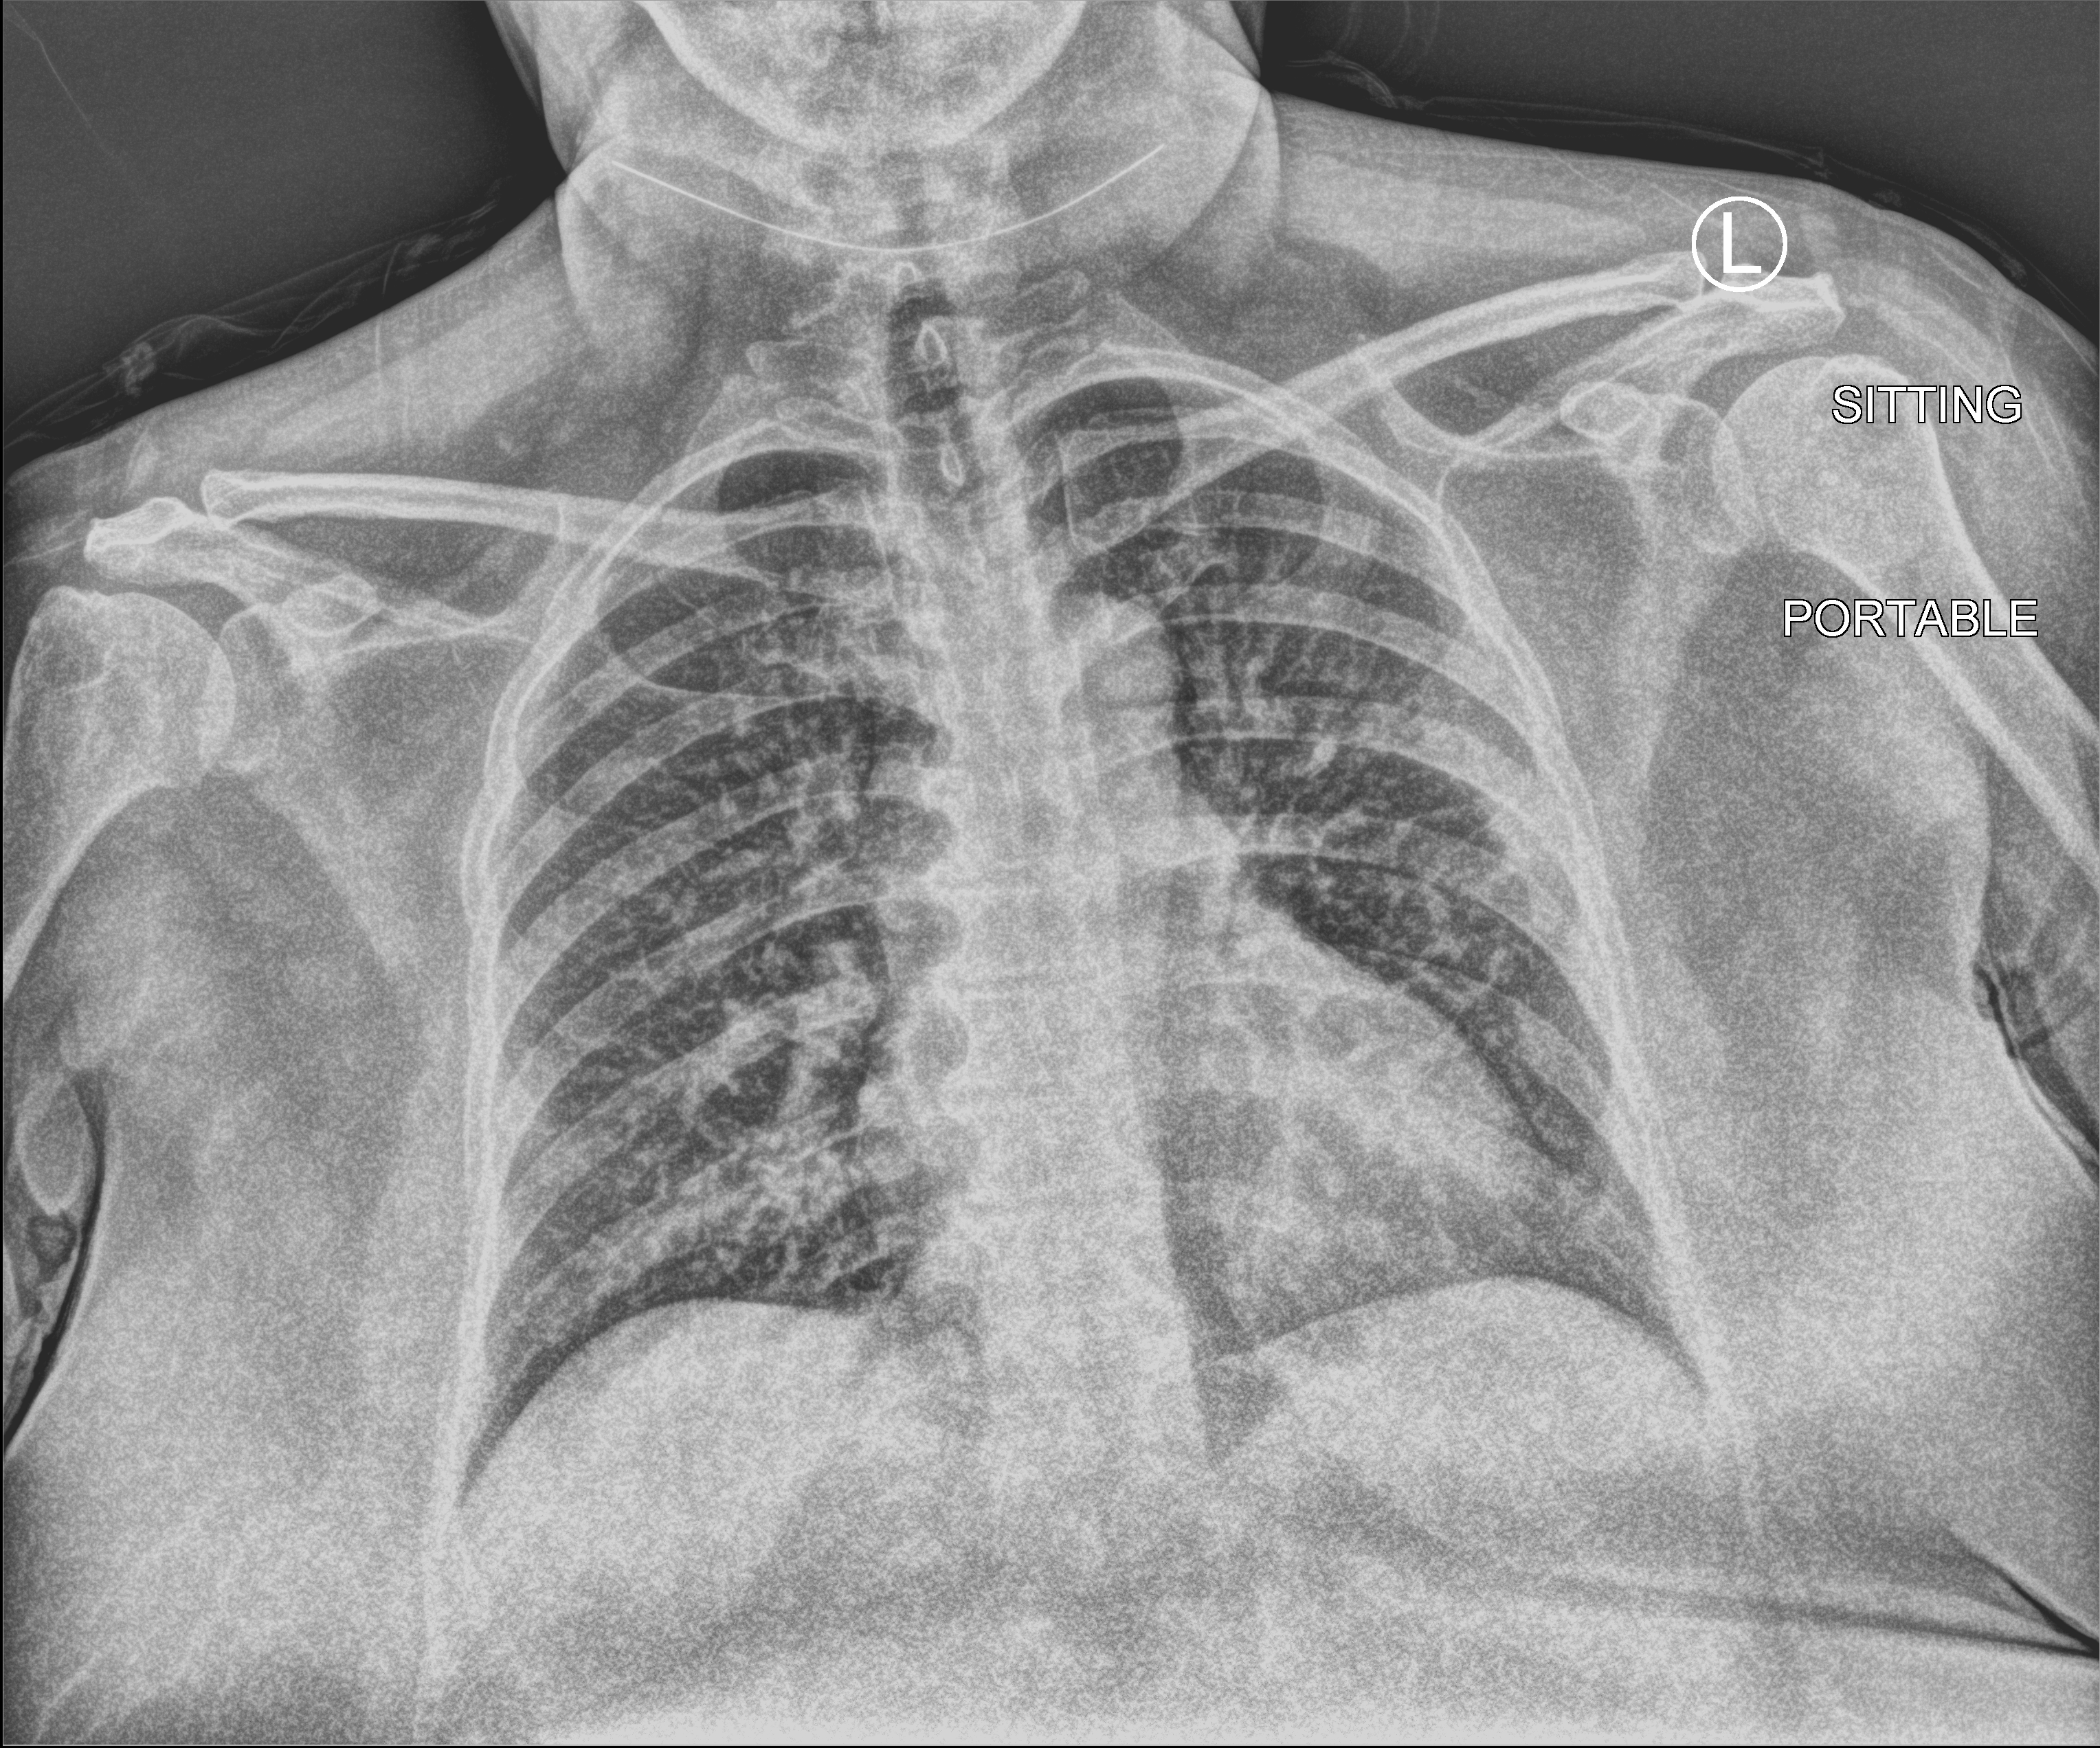
Portable chest radiograph; anteroposterior (AP) projection. Female patient hospitalised with COVID-19, age 18–59 years.
Hospital-stay facts (about this admission, not read from this image; timing relative to this image not recorded):
- mechanically ventilated during this hospital stay: no
- smoking status (admission record): never
- admitted to intensive care during this hospital stay: no